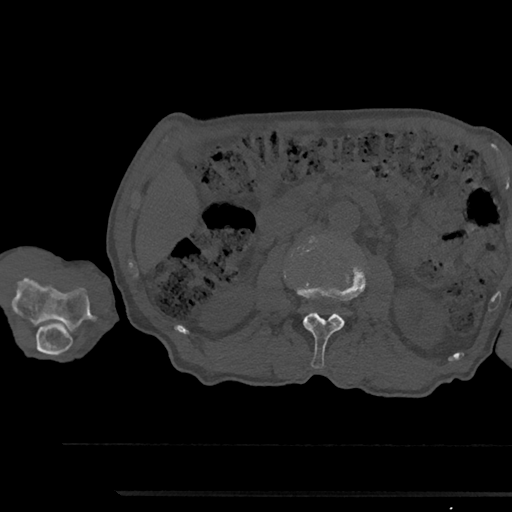
CT including the spine, one axial slice; slice 544 of 797 in the series (ordered by position); reconstruction kernel Br40s/3; bone window (W 1800 / L 400 HU); 0.5 mm slice thickness; 512 × 512 image matrix, field of view 367 × 367 mm. Patient: male, 79 years. Case-level facts recorded for this patient, not image findings: primary cancer: prostate.
Outlined on this slice (semi-automatic segmentation, software-assisted and operator-edited):
- L2 vertebra: bounding box <294,266,366,368> (left, top, right, bottom; pixels)